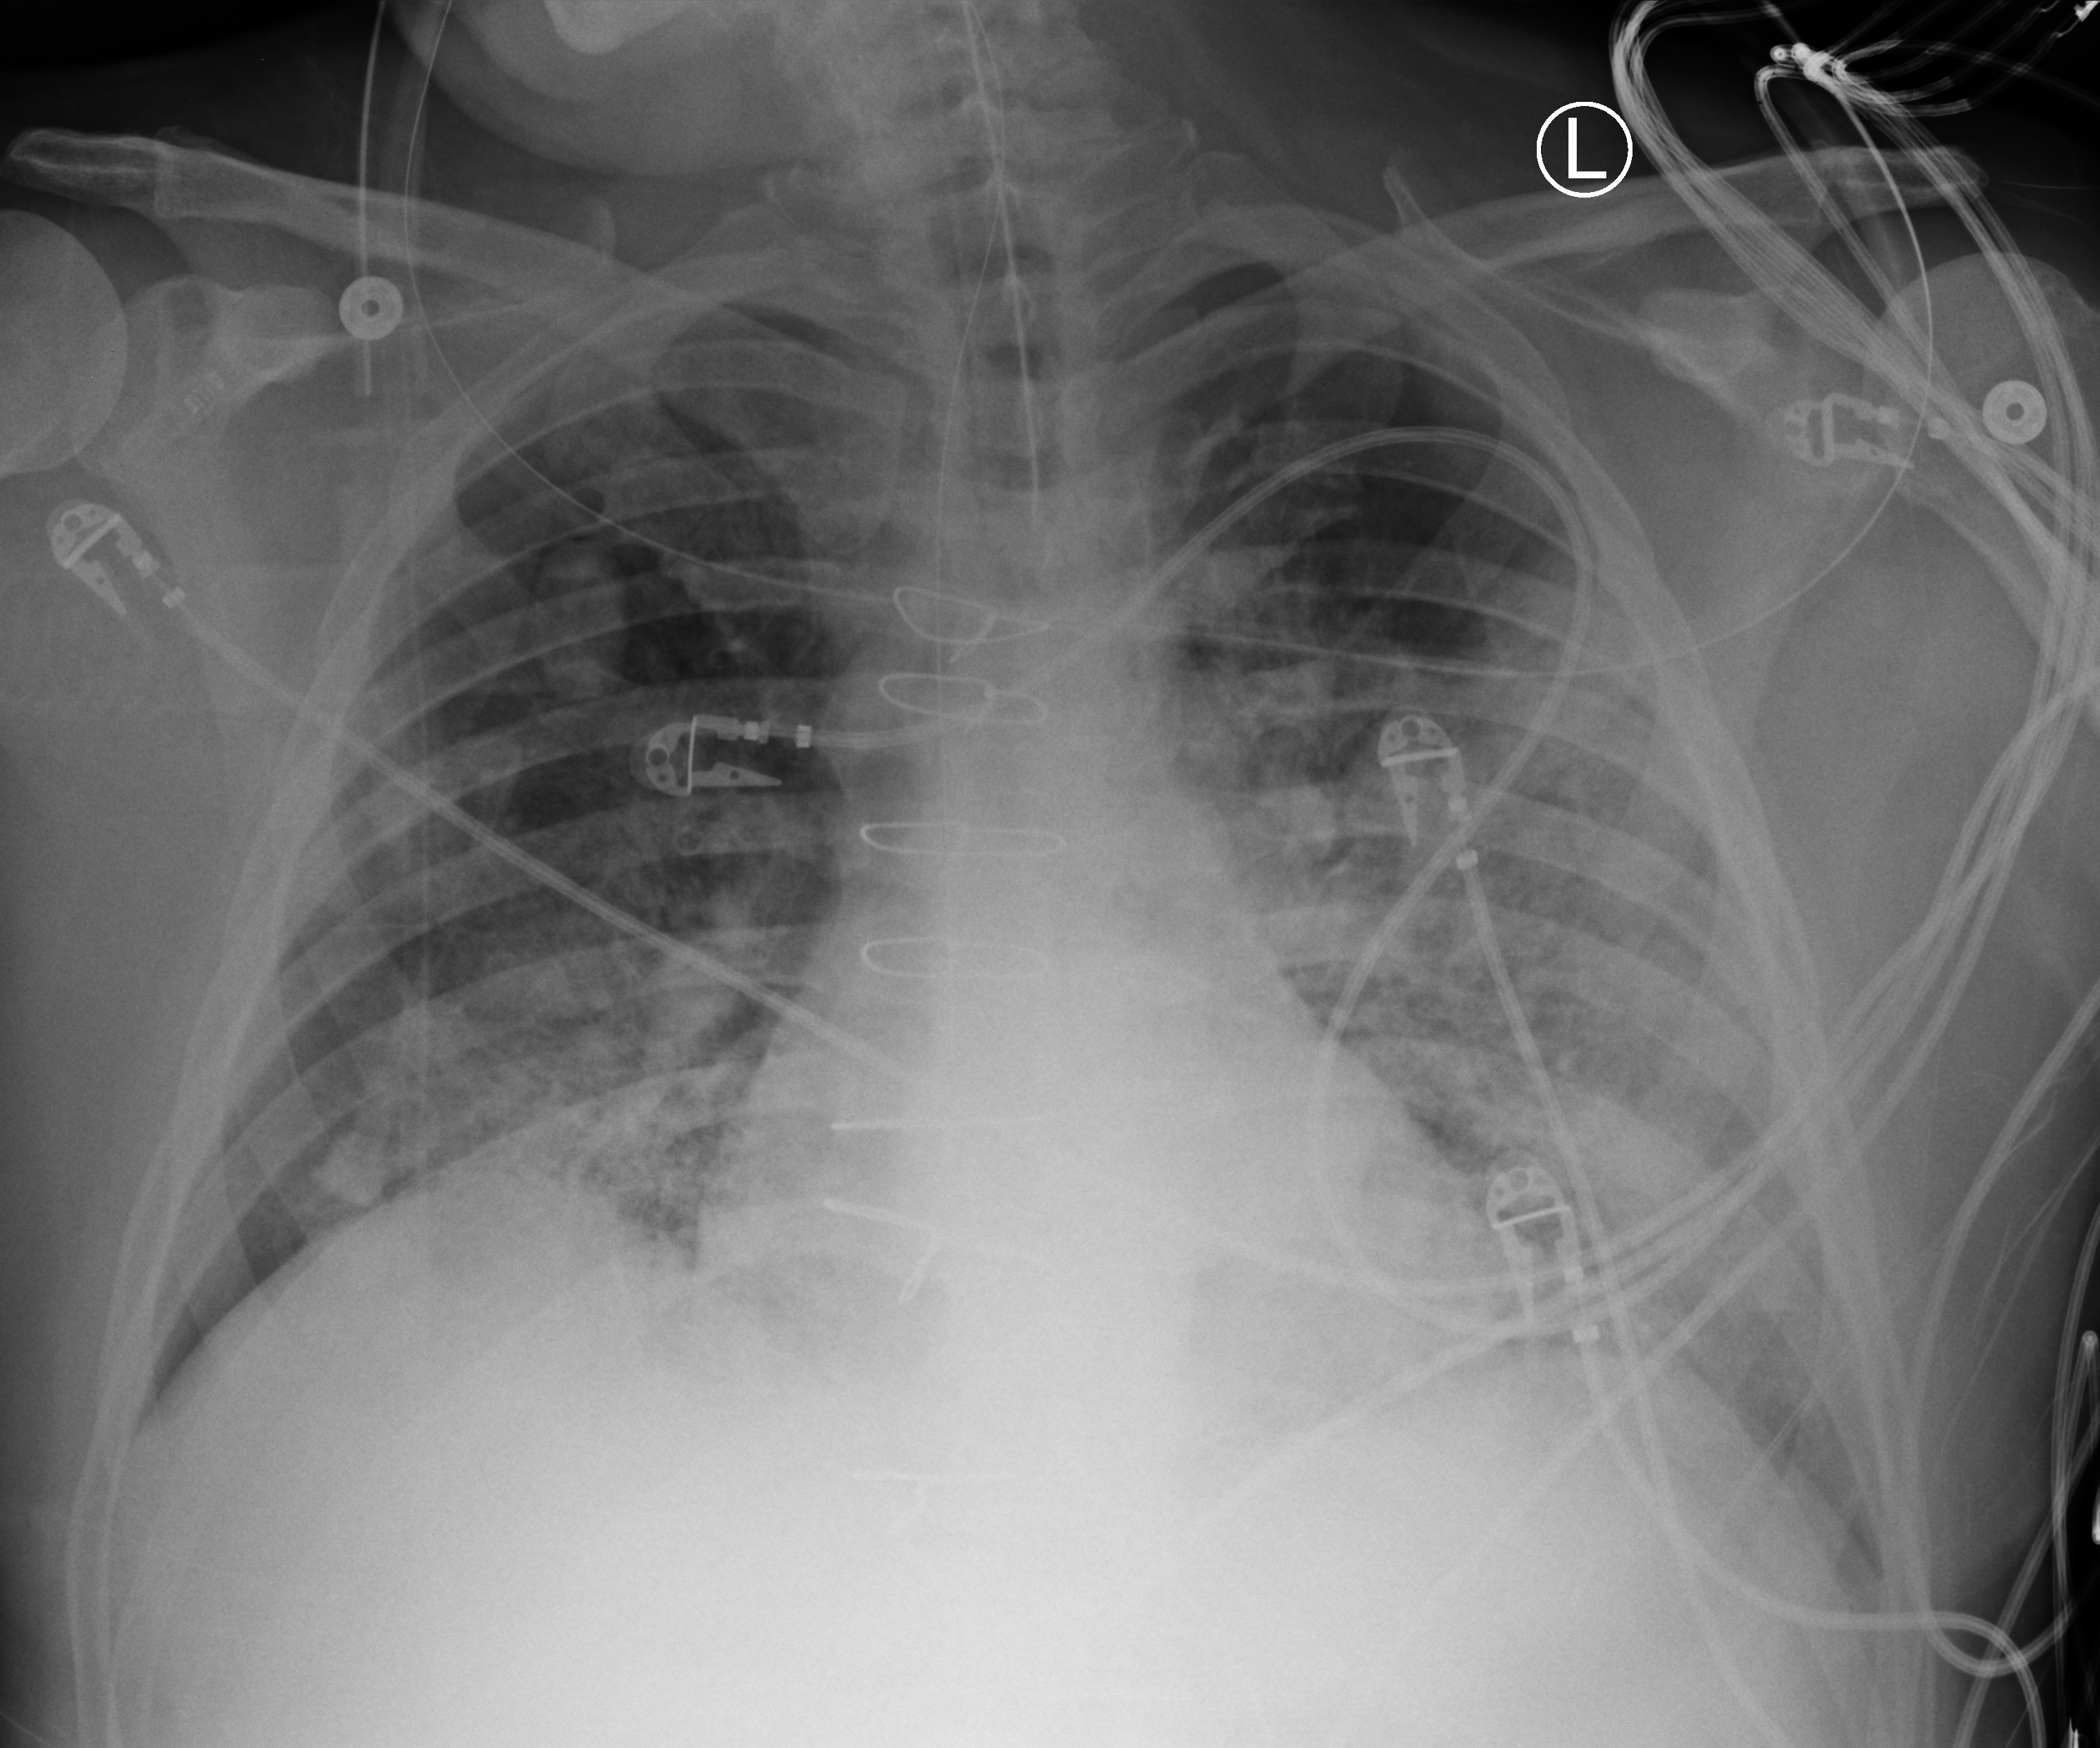
Portable chest radiograph. Male patient hospitalised with COVID-19, age 60–74 years.
Hospital-stay facts (about this admission, not read from this image; timing relative to this image not recorded): mechanically ventilated during this hospital stay: yes; admitted to intensive care during this hospital stay: yes; length of hospital stay: 44 days.